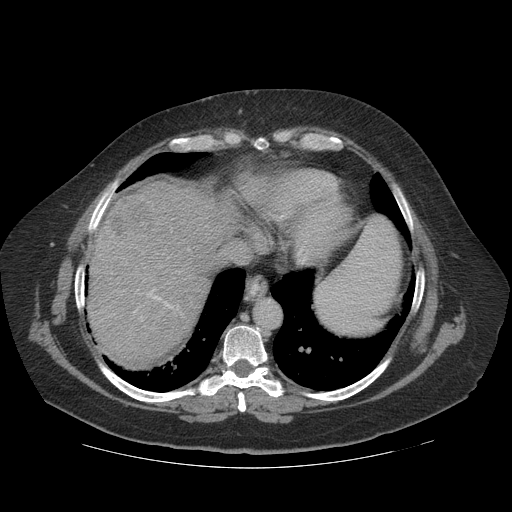
Contrast-enhanced abdominal CT (liver protocol), one axial slice; position 100 of 121 along the scan axis; 140 kVp; soft-tissue window (W 400 / L 40 HU); 2.5 mm slice thickness; 512 × 512 image matrix, field of view 420 × 420 mm. From the clinical record (not read from this slice): diagnosis: hepatocellular carcinoma (patient treated with transarterial chemoembolisation; whether this scan precedes or follows treatment is not stated here); TNM stage (as recorded): Stage-IIIA.
Outlined on this slice (semi-automatic segmentation, software-assisted and operator-edited):
- abdominal aorta: box from (x=255, y=300) to (x=281, y=330) px
- liver parenchyma outside the tumour (the mass and vessels are separate outlines, so this box may not span the whole liver): (x=88, y=182)–(x=244, y=366)
- mass: (x=109, y=195)–(x=165, y=245)
- liver vessels: (x=134, y=290)–(x=173, y=321)